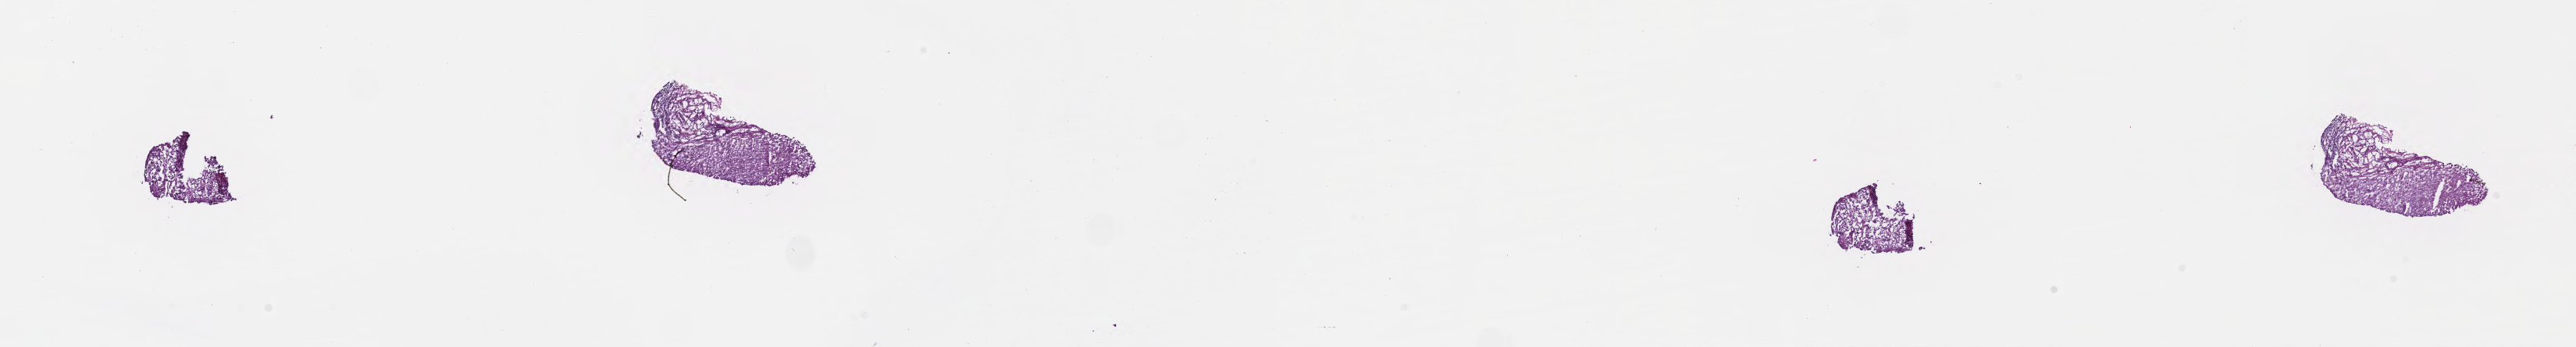
H&E whole-slide image — a low-resolution overview of the entire scanned area, about 26.7 x 3.6 mm. Frozen section. Specimen: metastatic tumor tissue, resected from liver. Male, age 51 years at initial diagnosis. Slide review estimates, as recorded: tumor cells 50%, tumor nuclei 40%, stromal cells 0%, necrosis 0%, normal cells 50%. Infiltration values recorded for this section: lymphocyte infiltration 0%, monocyte infiltration 0%, neutrophil infiltration 0%.
* patient diagnosis (primary): Adenocarcinoma, NOS